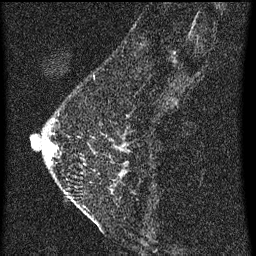
Breast MRI (dynamic contrast-enhanced), one sagittal slice; position 20 of 60 along the scan axis; dynamic contrast-enhanced series, image 2 of 3 at this slice position (ordered by acquisition); 1.5 T; TE 4.2 ms, TR 8 ms; 256 × 256 image matrix, field of view 180 × 180 mm. Female patient, age 47 years.
Structures marked on this image (semi-automatic segmentation, software-assisted and operator-edited):
- analysis volume of interest (the breast-tissue region the enhancement analysis was run in; not a lesion): bounding box [x1, y1, x2, y2] px = [42, 92, 137, 199]
- tumour enhancement mask (voxels above the 70 % enhancement threshold inside the analysis volume of interest): [50, 144, 126, 173]